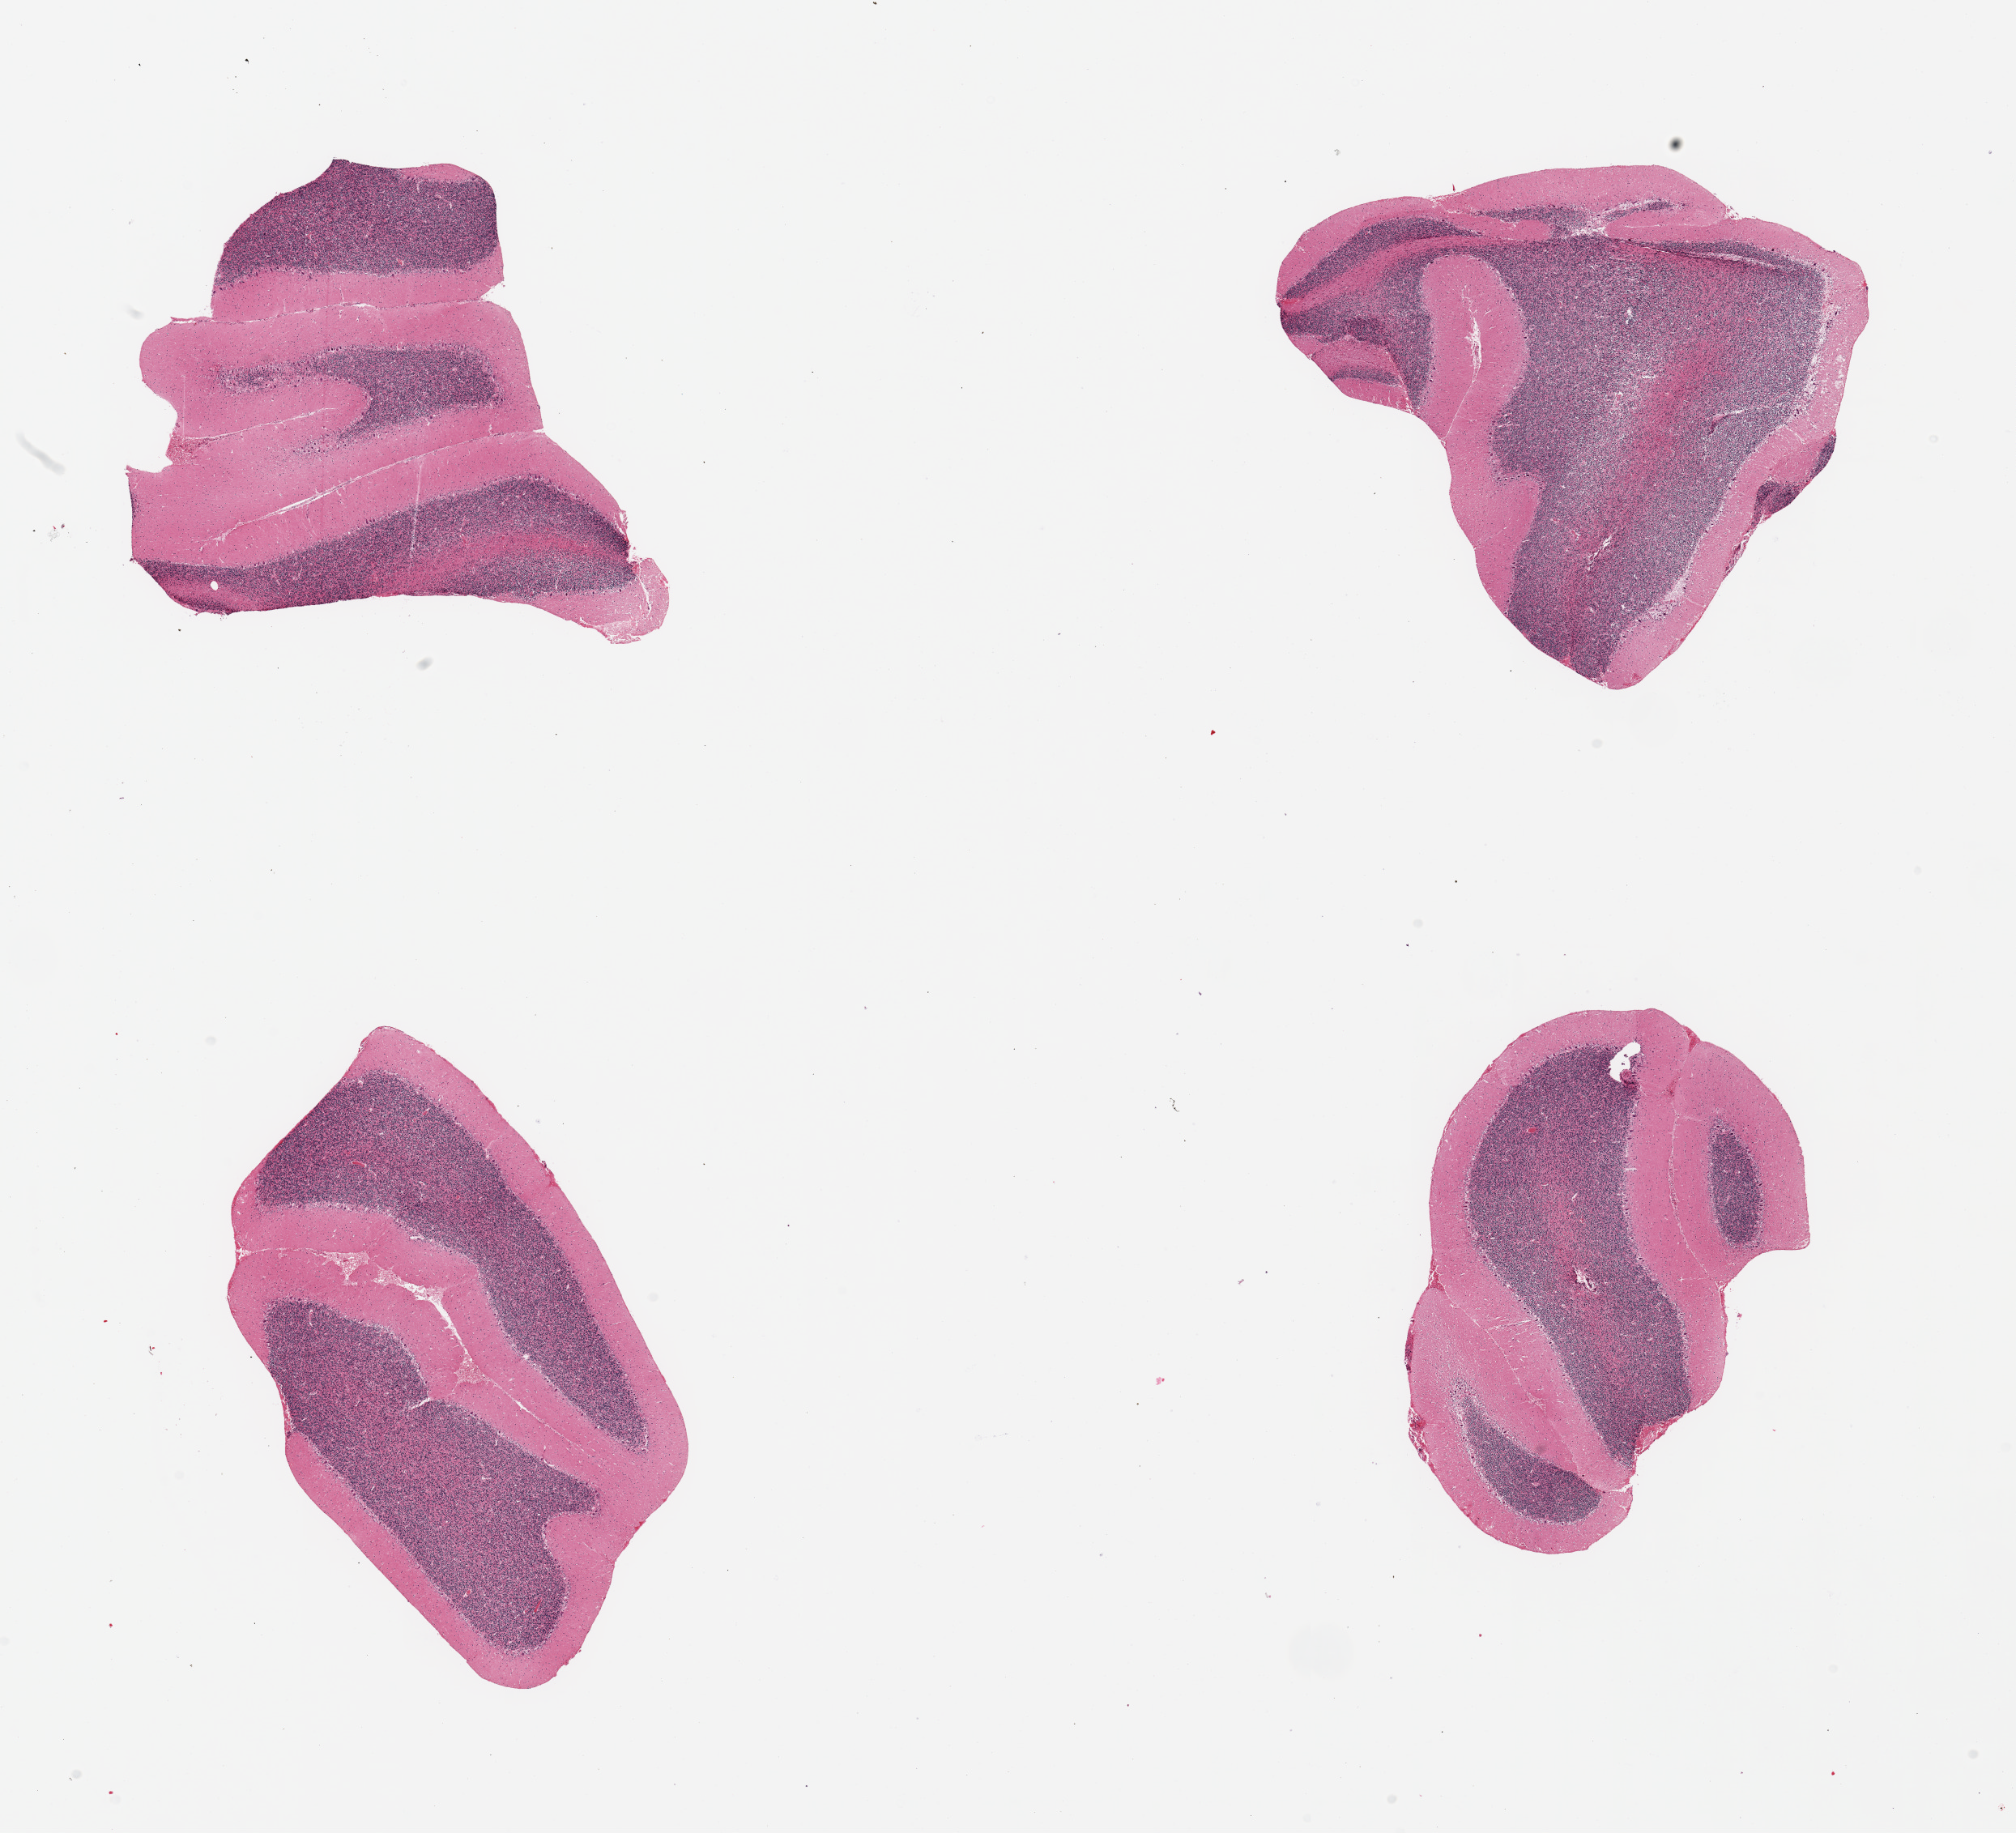
Haematoxylin and eosin whole-slide image — shown as a low-resolution overview of the whole scanned area (about 19.7 x 17.9 mm). PAXgene-fixed, paraffin-embedded tissue. Section of cerebellum (target tissue). Donor tissue sample. Female donor.
* reviewer comment on this tissue sample: 4 pieces